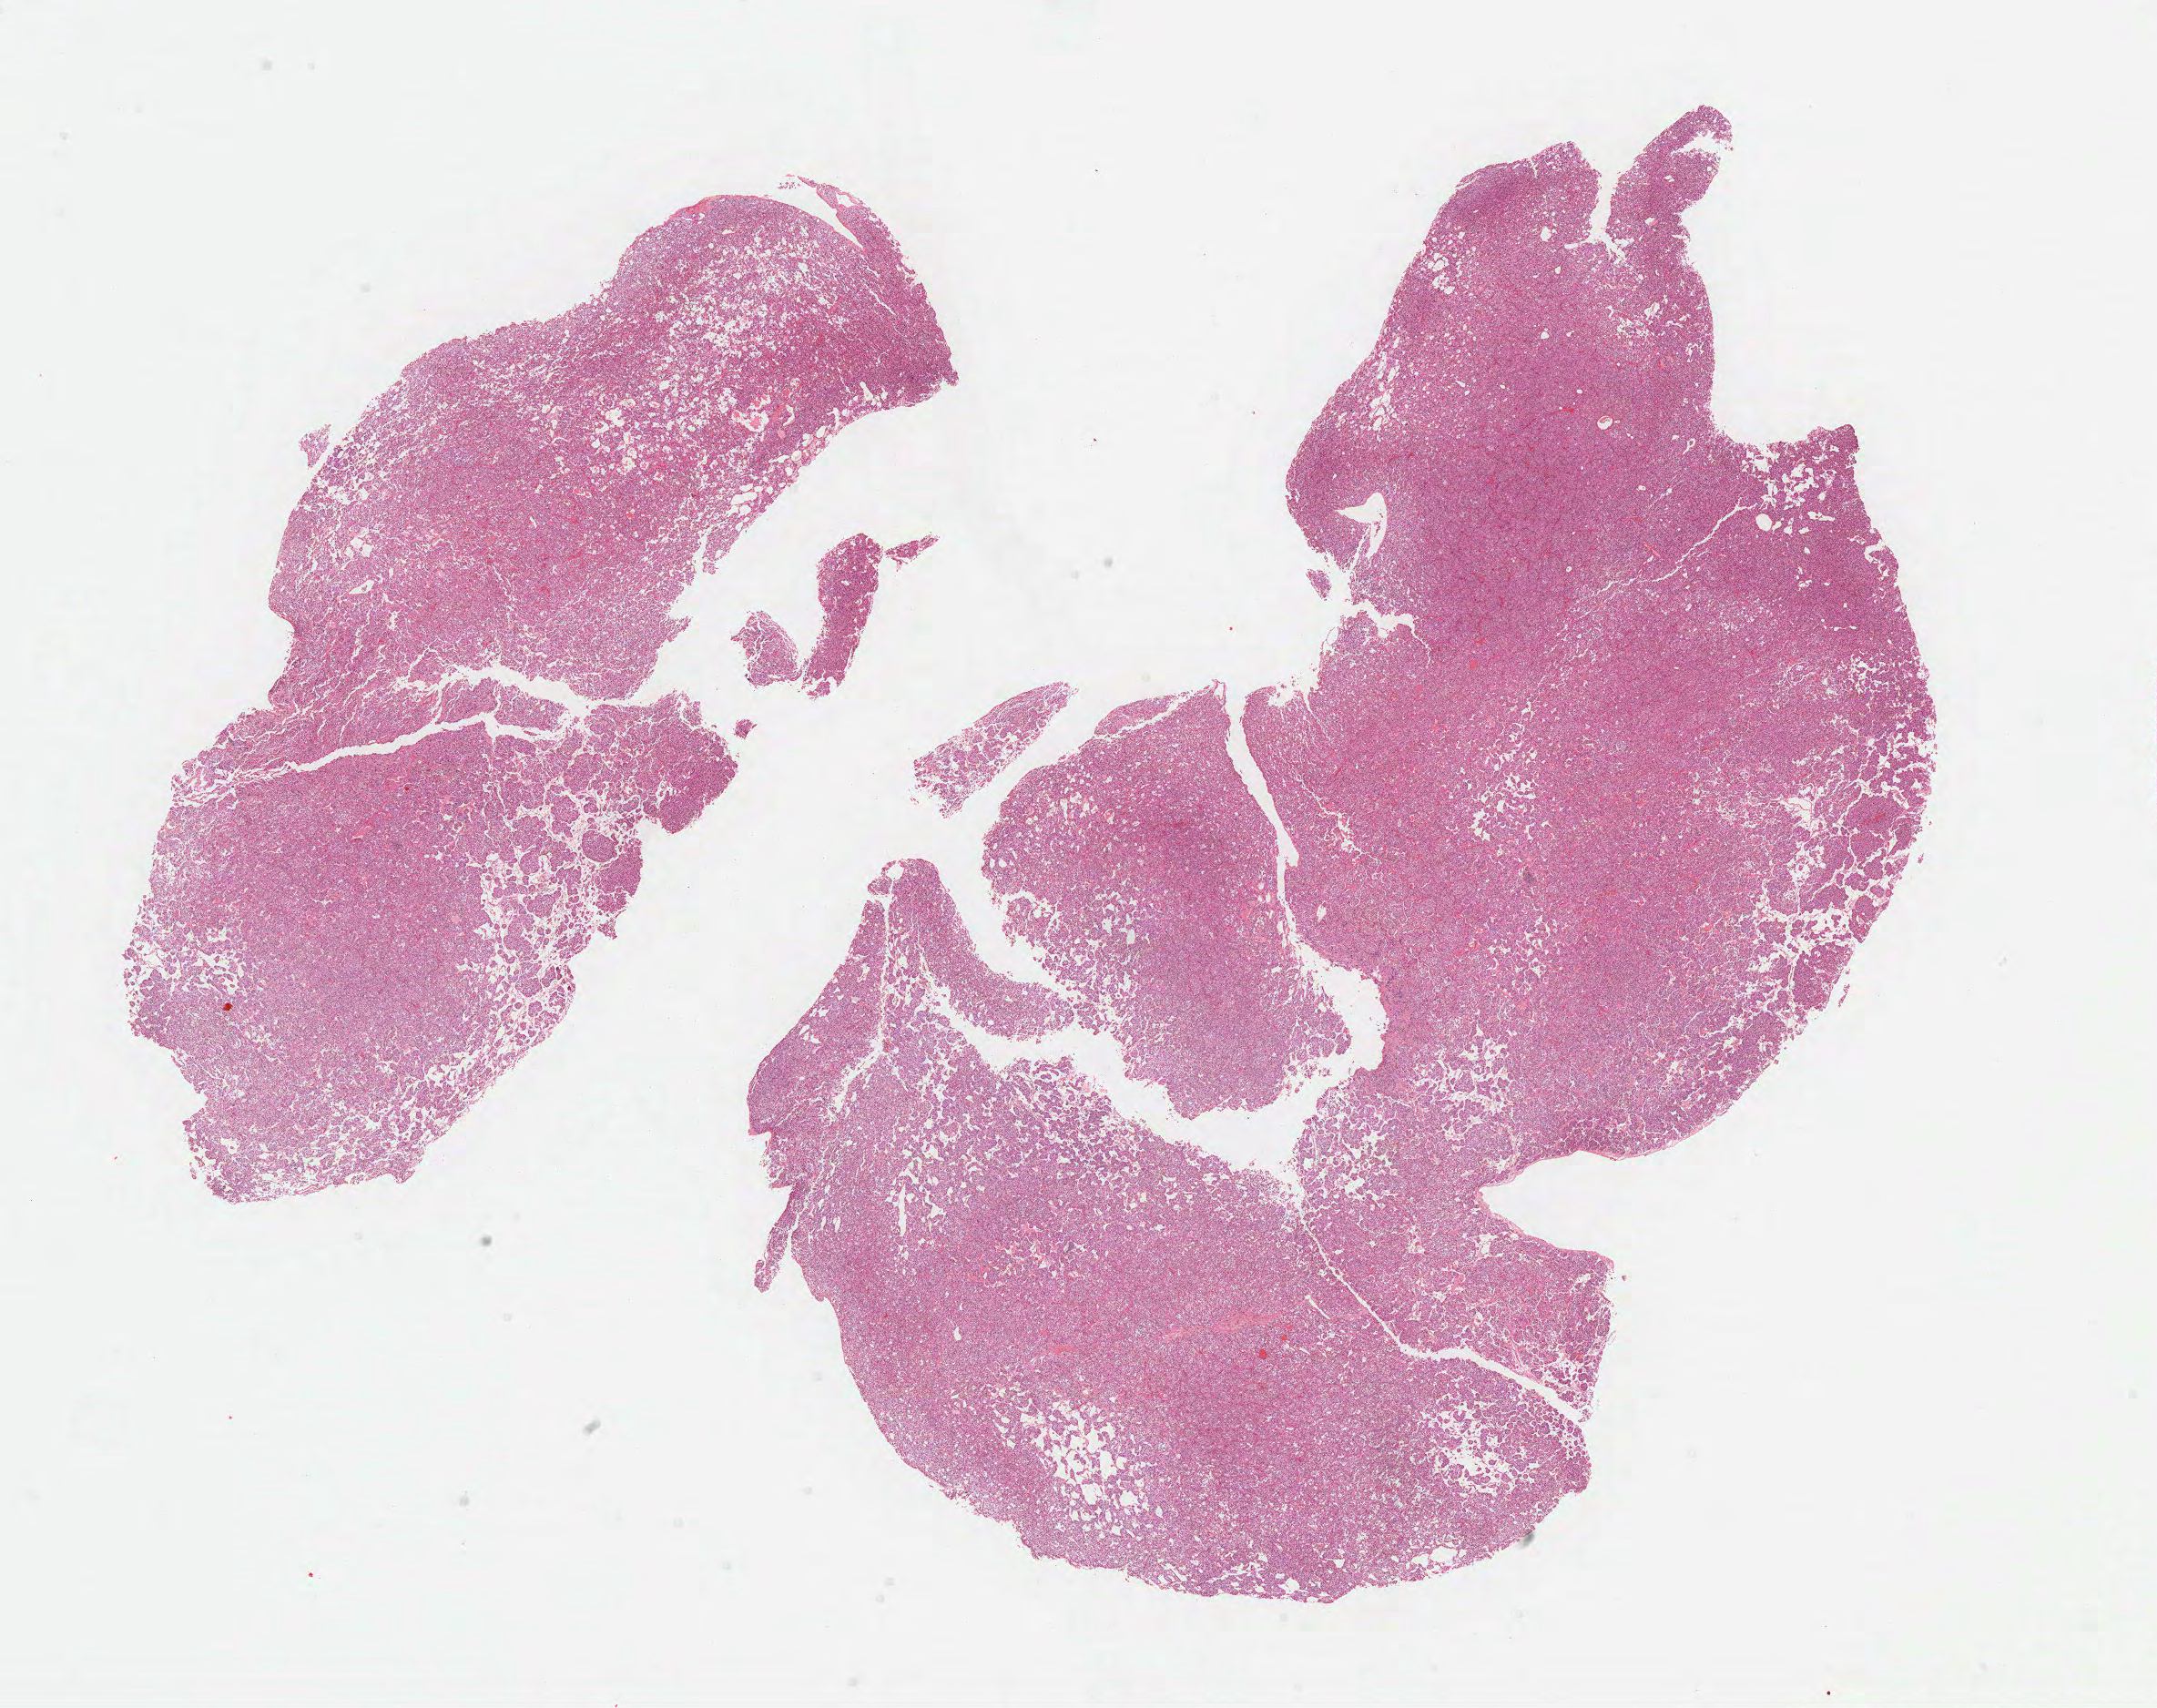
Hematoxylin and eosin (H&E) stained whole-slide image, a low-resolution overview of the entire scanned area, about 19.1 x 15.2 mm (acquisition: 40x scan). Formalin-fixed paraffin-embedded (FFPE) diagnostic section. Pancreas, primary tumour sample. Patient: male, age at initial diagnosis 65 years. Histologic grade: G1 (well differentiated).
- diagnosis: Neuroendocrine carcinoma, NOS (head of pancreas)
- AJCC pathologic stage: IB (6th edition)
- lymph nodes positive (case pathology): 0 of 16 examined